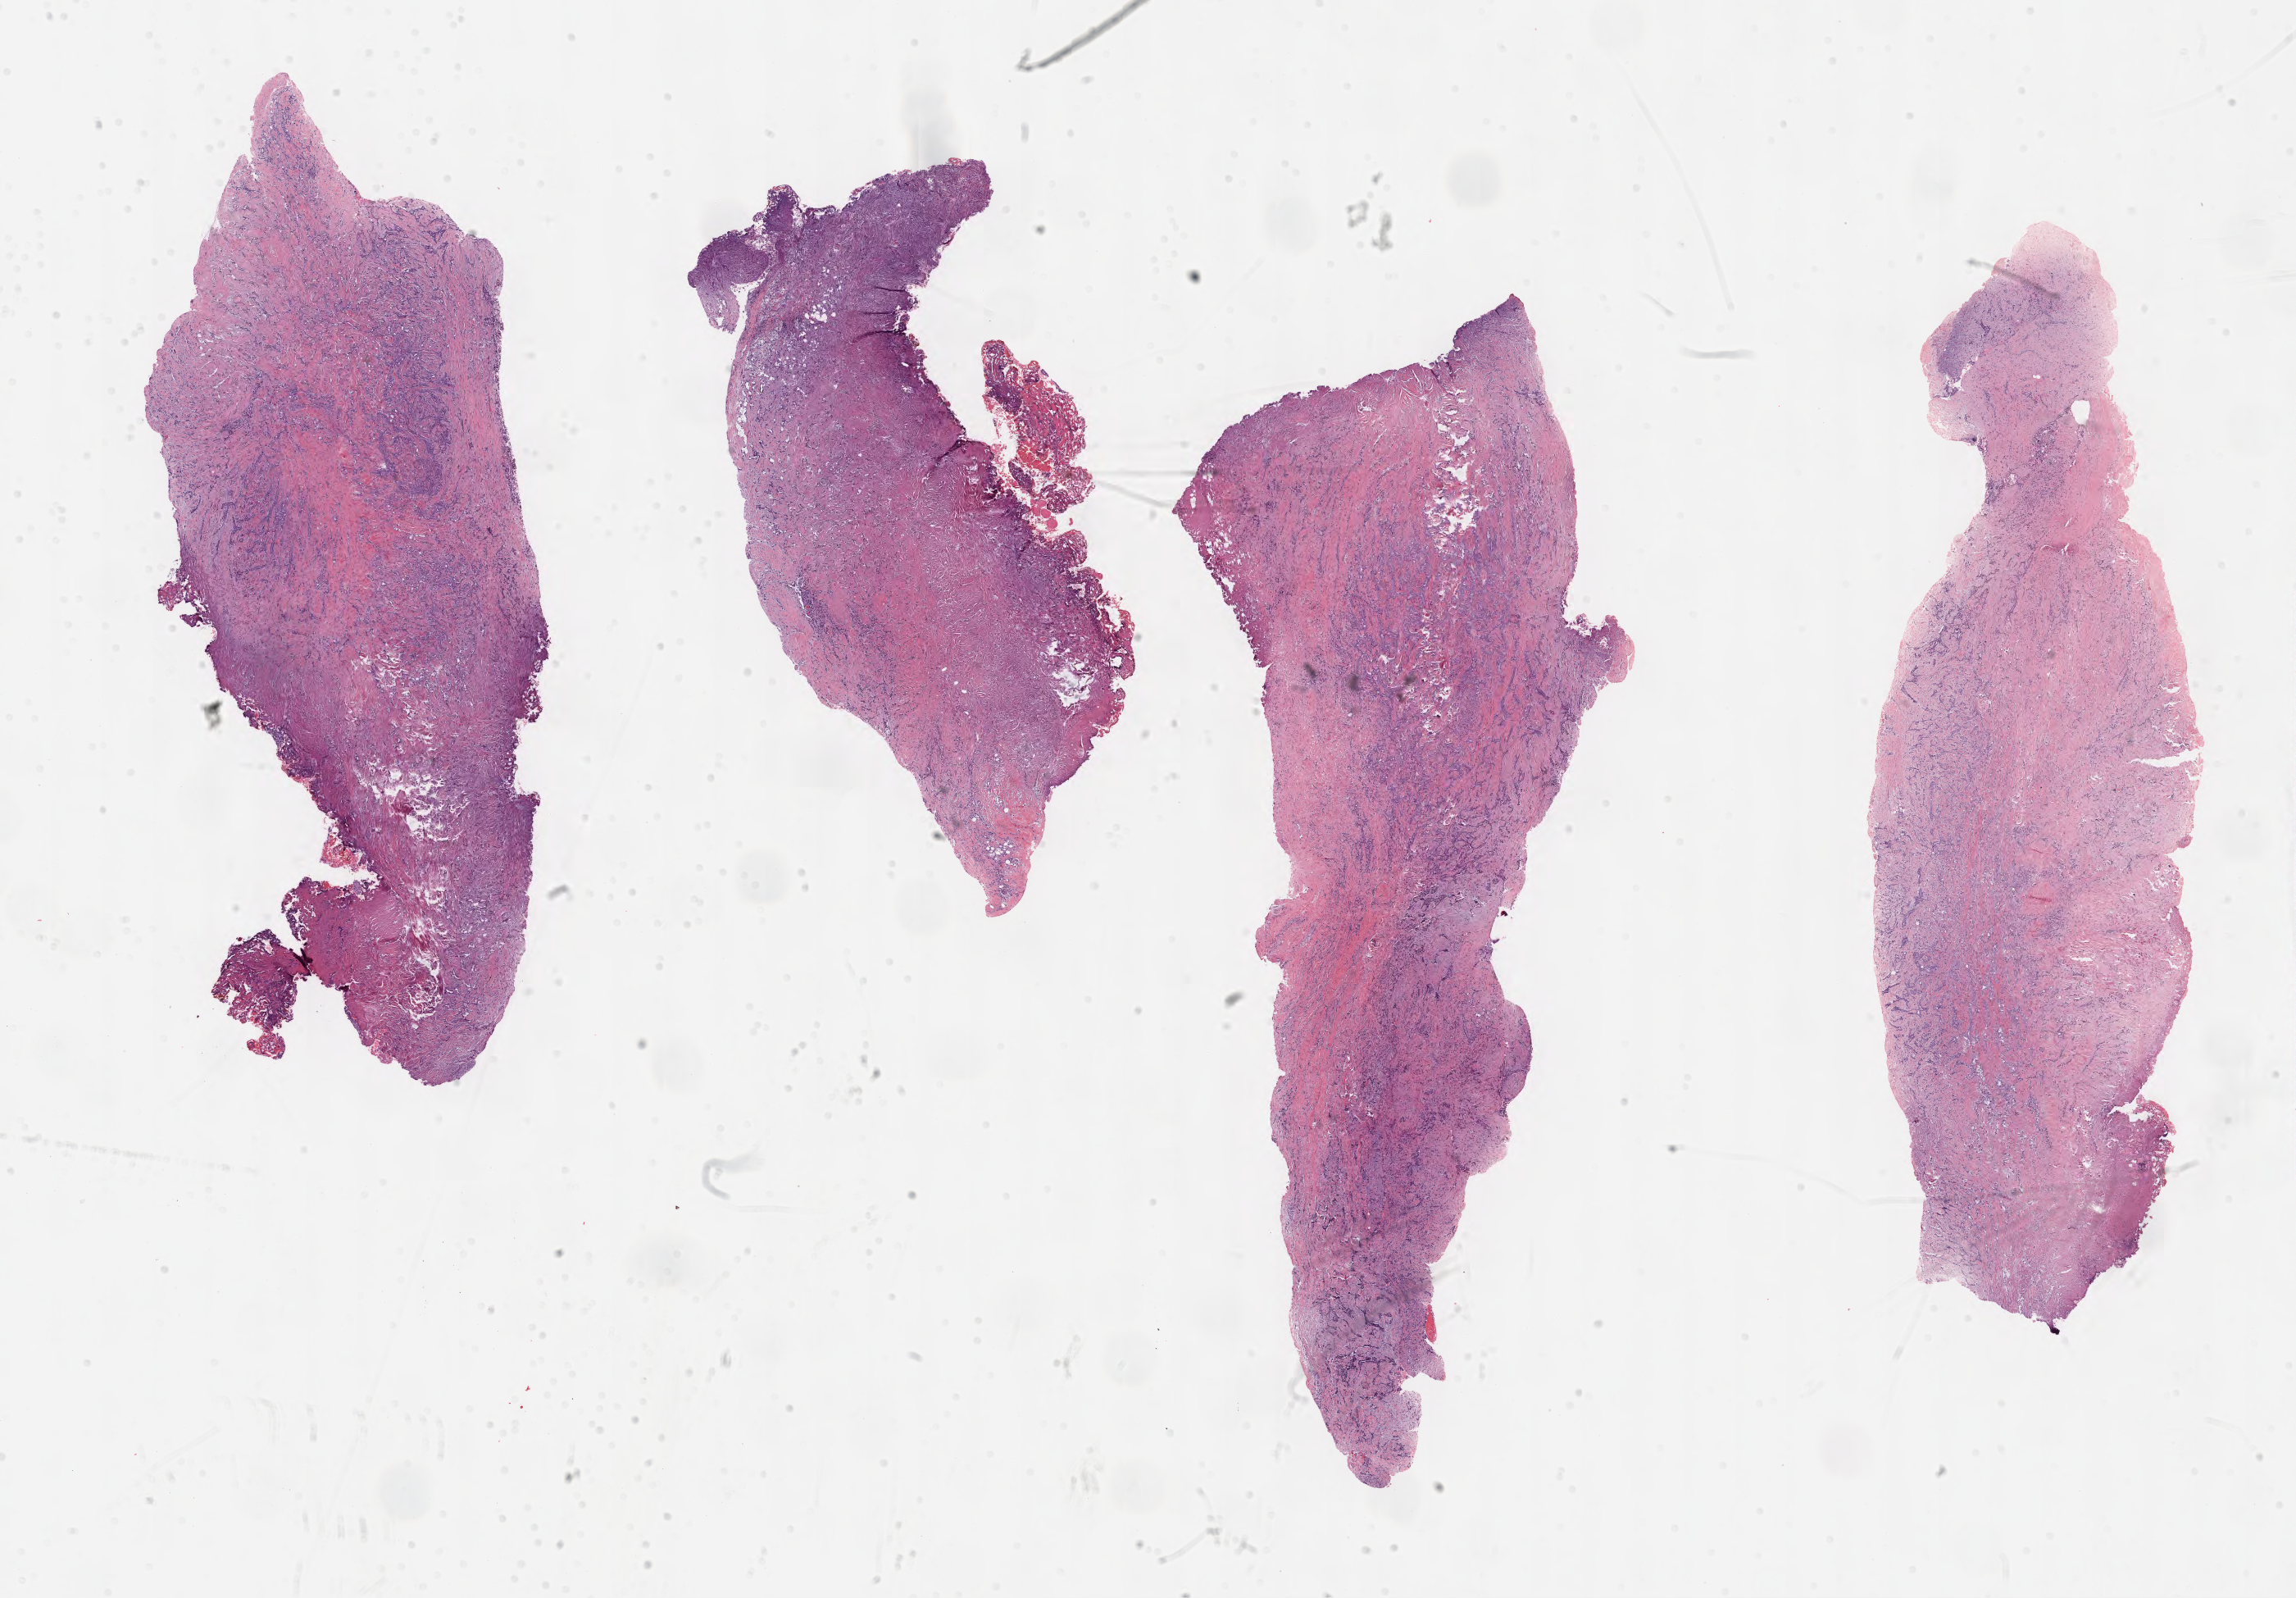
Digitized H&E-stained tissue section (whole slide) — whole scanned area (about 22.6 x 15.7 mm, acquisition: 40x scan) shown as a low-resolution overview. FFPE section. Primary tumour sample from the mesothelium. Male, age 69 years at initial diagnosis.
* AJCC pathologic stage: II (6th edition)
* laterality: right
* histologic diagnosis: Epithelioid mesothelioma, malignant